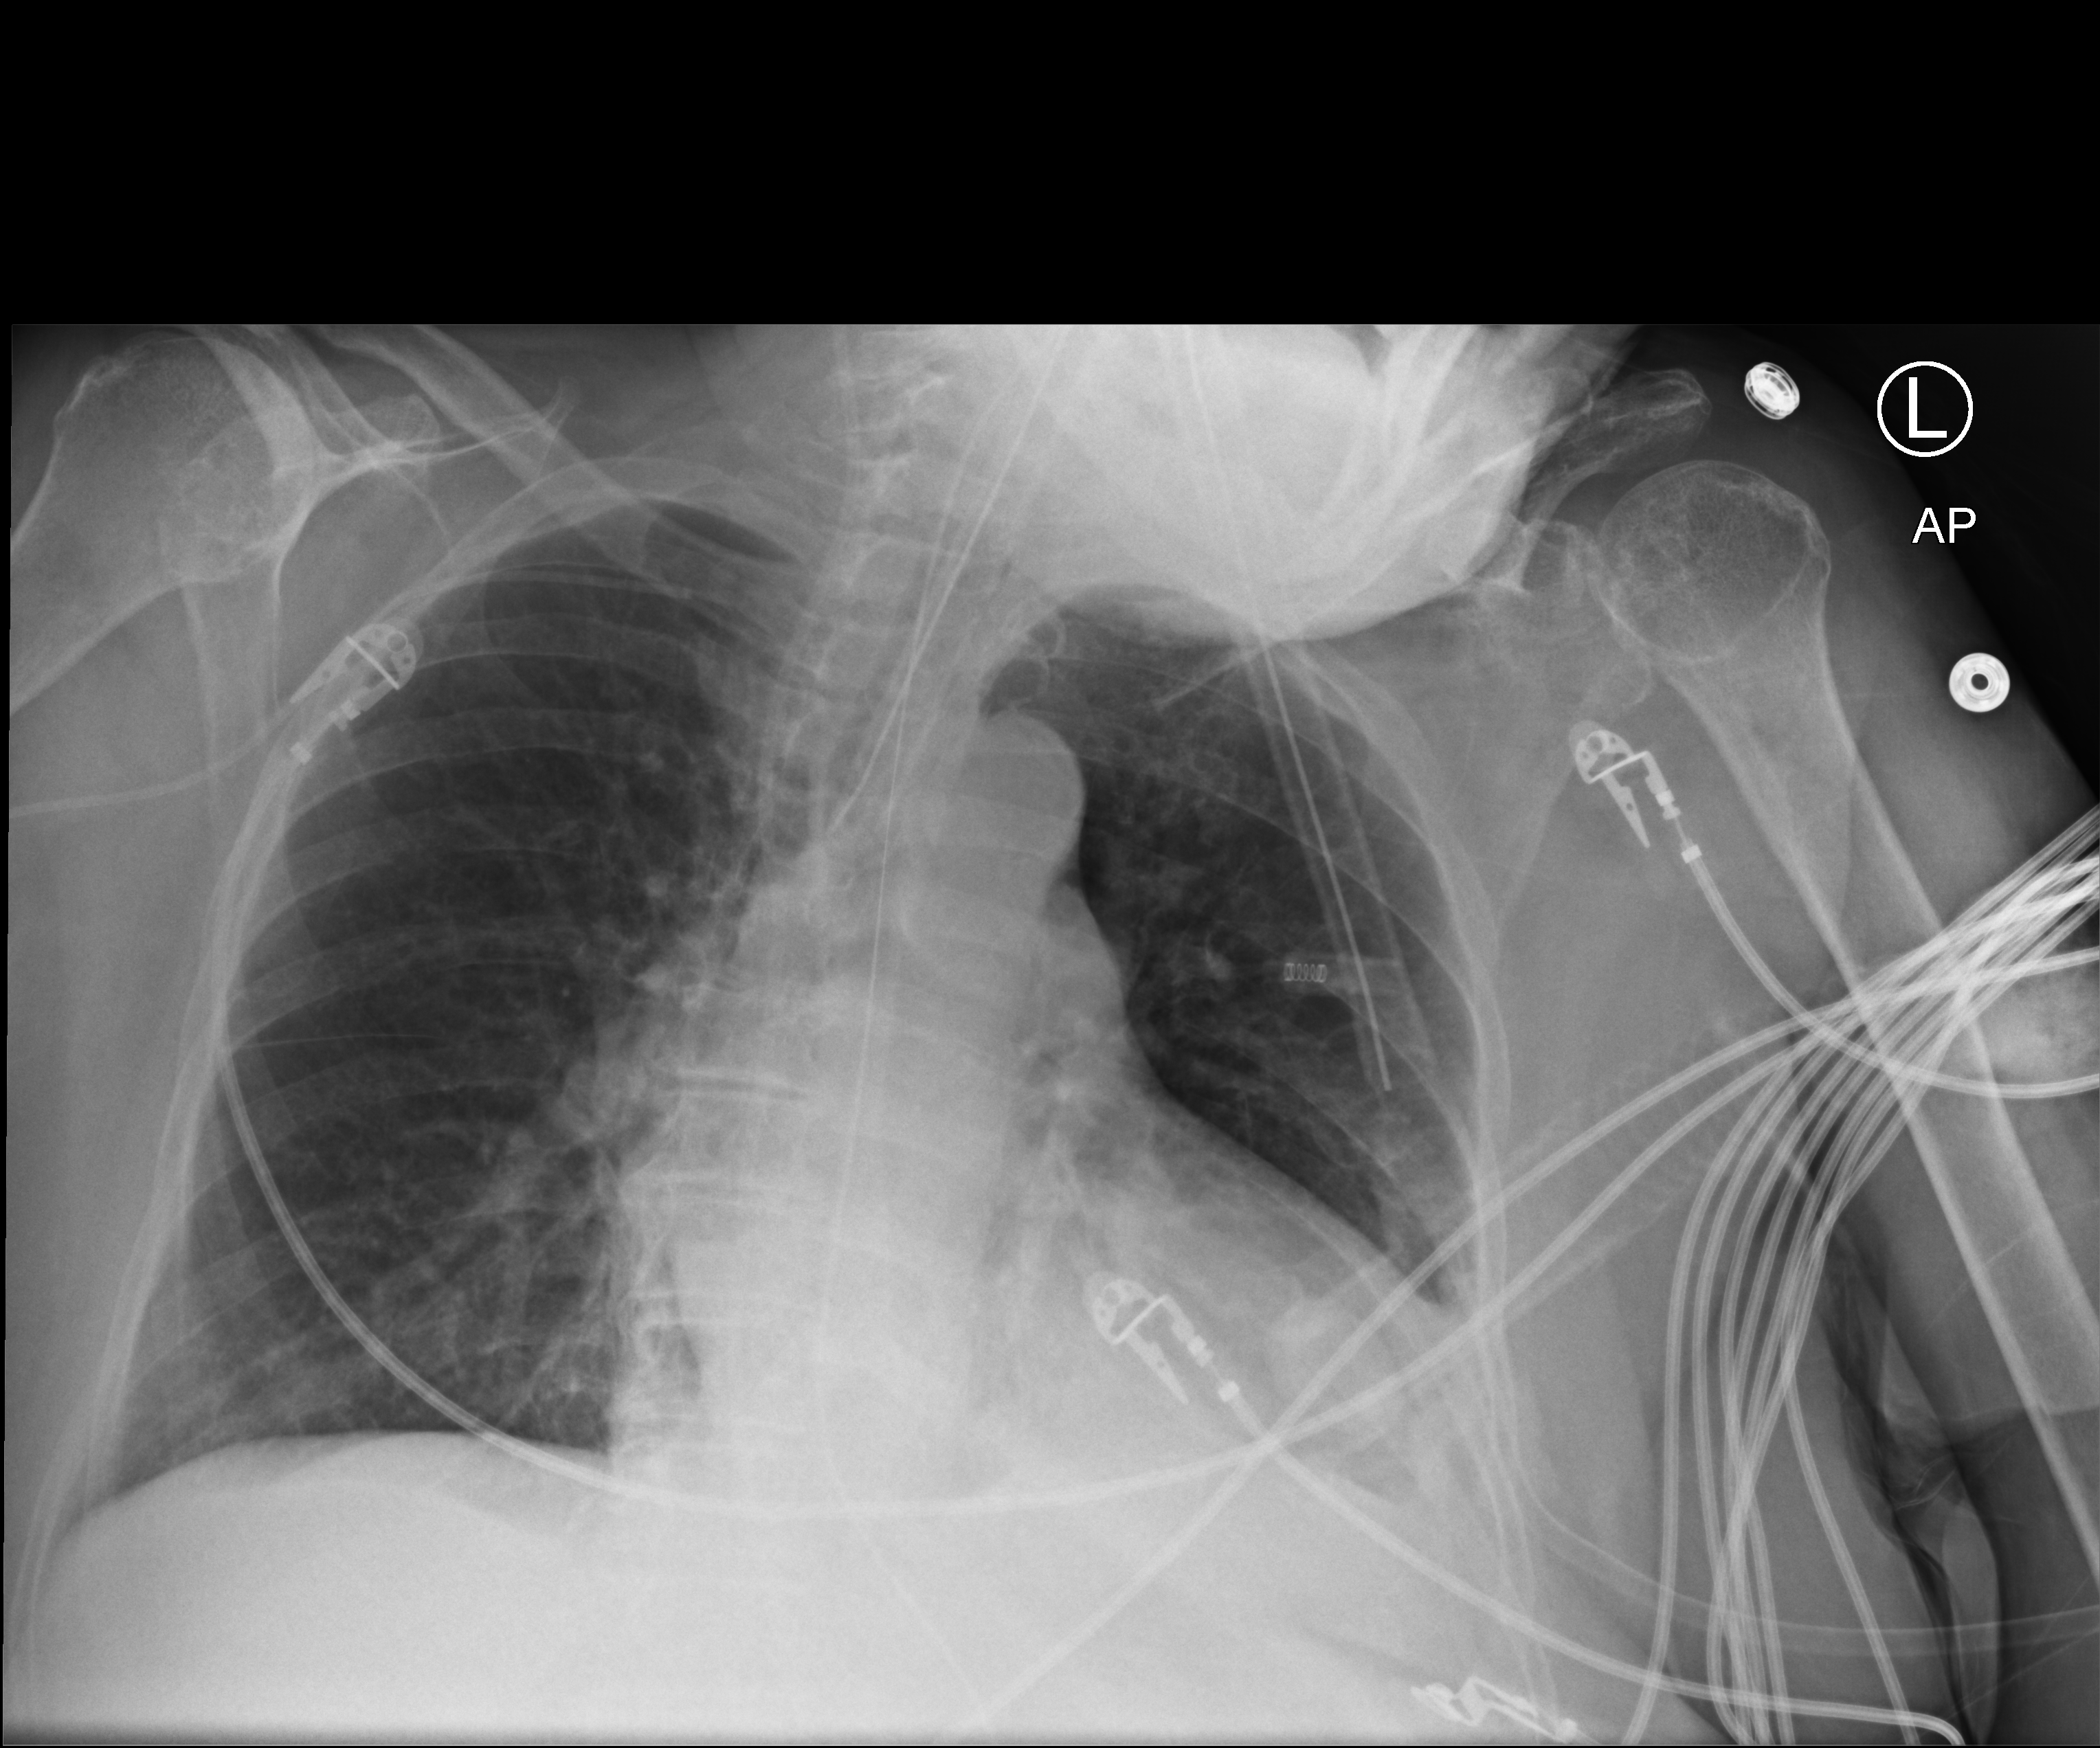
Chest X-ray (portable). Female patient hospitalised with COVID-19, age 75–90 years.
From the hospital-stay record, not from the radiograph (when in the stay this image was taken is not recorded): admitted to intensive care during this hospital stay: yes; diabetes (admission record): yes.